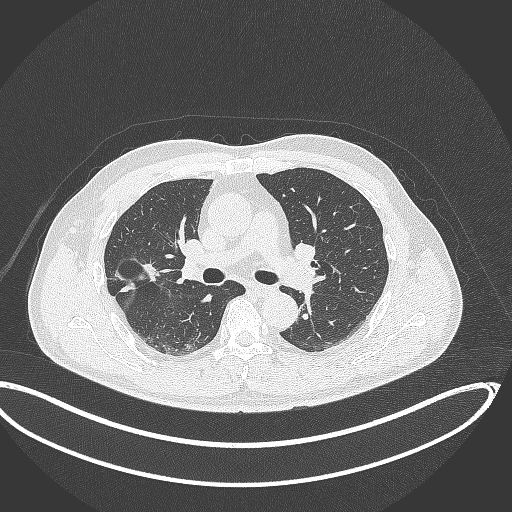
Chest CT, one axial slice. Position 204 of 391 along the scan axis. Reconstruction kernel B70f. 120 kVp. Lung window (W 1500 / L -600 HU). 1 mm slice thickness. 512 × 512 image matrix, field of view 439 × 439 mm. Patient: male, 63 years. From the clinical record (not read from this slice): clinical TNM (as recorded): T1c N0 M0.
Structures marked on this image (rectangle marked by the reading radiologist):
- lung tumour (recorded histology: adenocarcinoma): bounding box (x1, y1, x2, y2) in pixels: (111, 253, 165, 296)